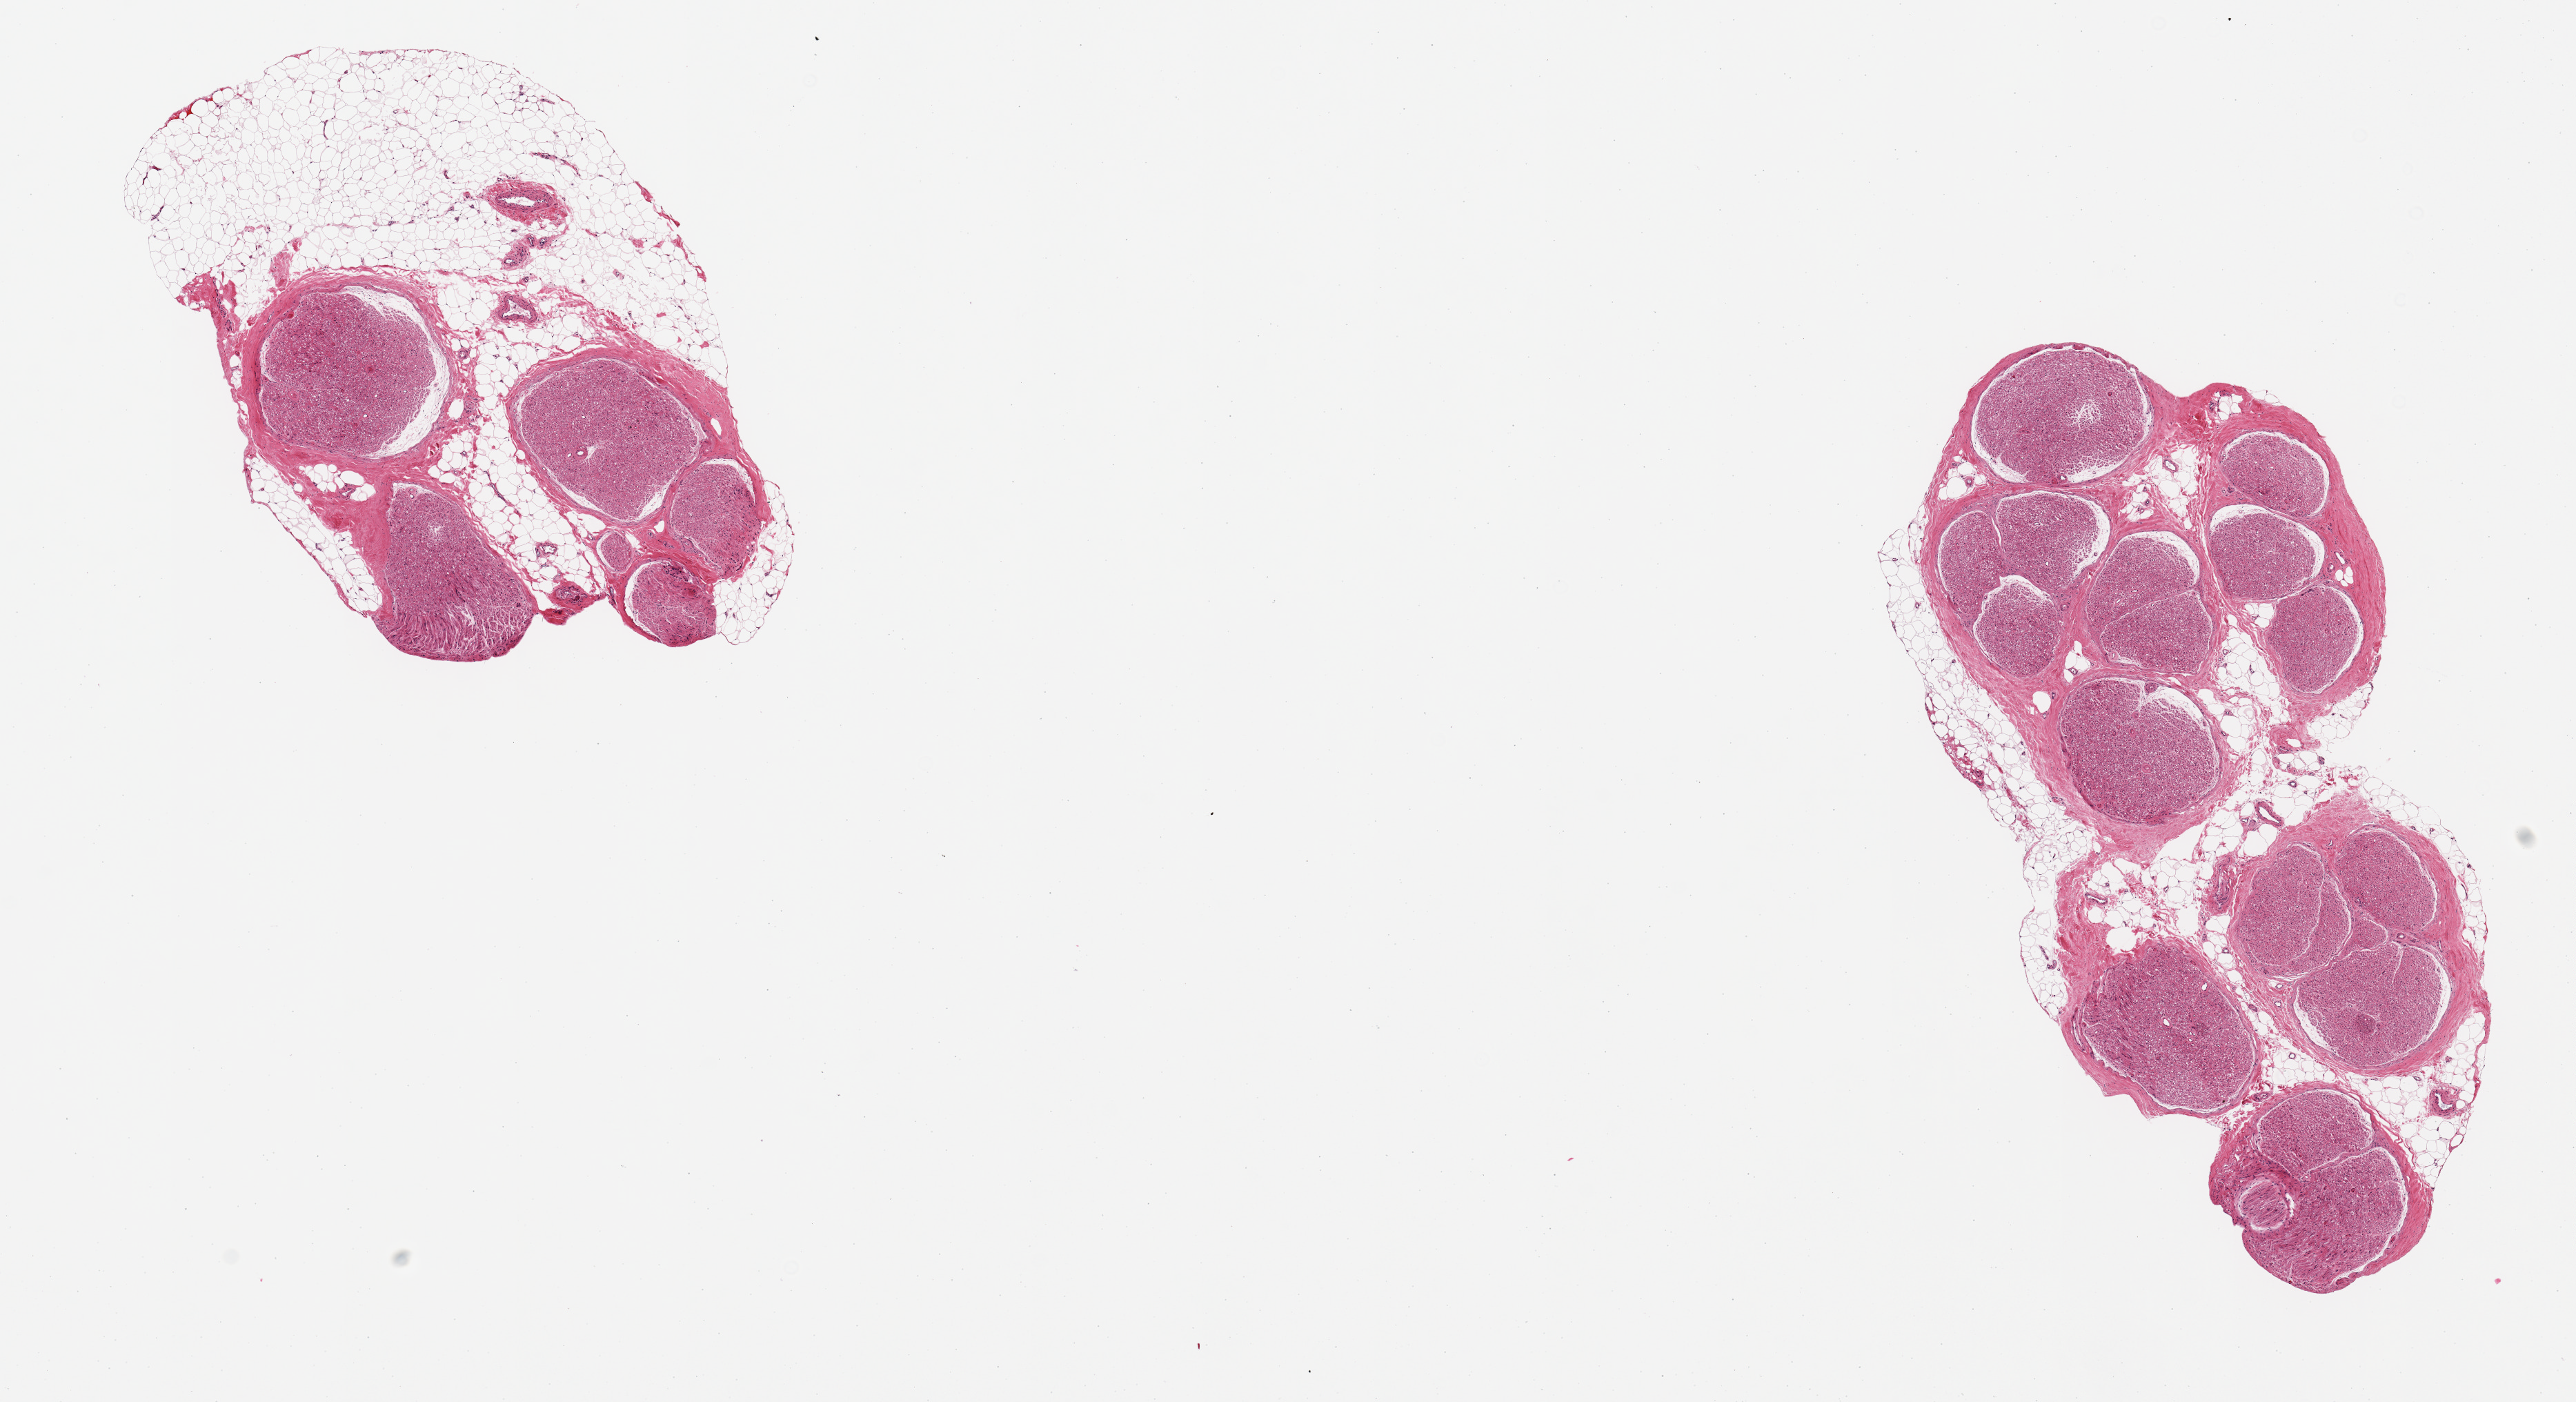
Whole-slide image, H&E stain, brightfield, a low-resolution overview of the entire scanned area, about 14.8 x 8.0 mm; PAXgene-fixed paraffin-embedded (PFPE) section; sampled site (target tissue): tibial nerve; donor tissue sample. Donor sex: male.
- pathologist's review note for this sample: 2 pieces, nubbing adherent fat, ~1.5 mm, one section